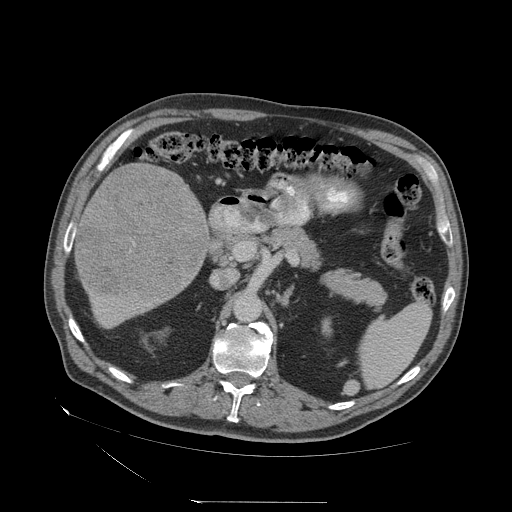
Contrast-enhanced abdominal CT (liver protocol), one axial slice; slice 21 of 83 in the series (ordered by position); soft-tissue window (W 400 / L 40 HU); 512 × 512 image matrix, field of view 460 × 460 mm. Case-level facts recorded for this patient, not image findings: diagnosis: hepatocellular carcinoma (patient treated with transarterial chemoembolisation; whether this scan precedes or follows treatment is not stated here); TNM stage (as recorded): Stage-I; Child-Pugh class: A; tumour differentiation: well differentiated; tumour nodularity: uninodular.
Outlined on this slice (semi-automatic segmentation, software-assisted and operator-edited):
- liver parenchyma outside the tumour (the mass and vessels are separate outlines, so this box may not span the whole liver): bounding box [x1, y1, x2, y2] px = [74, 162, 208, 326]
- mass: [76, 163, 207, 299]